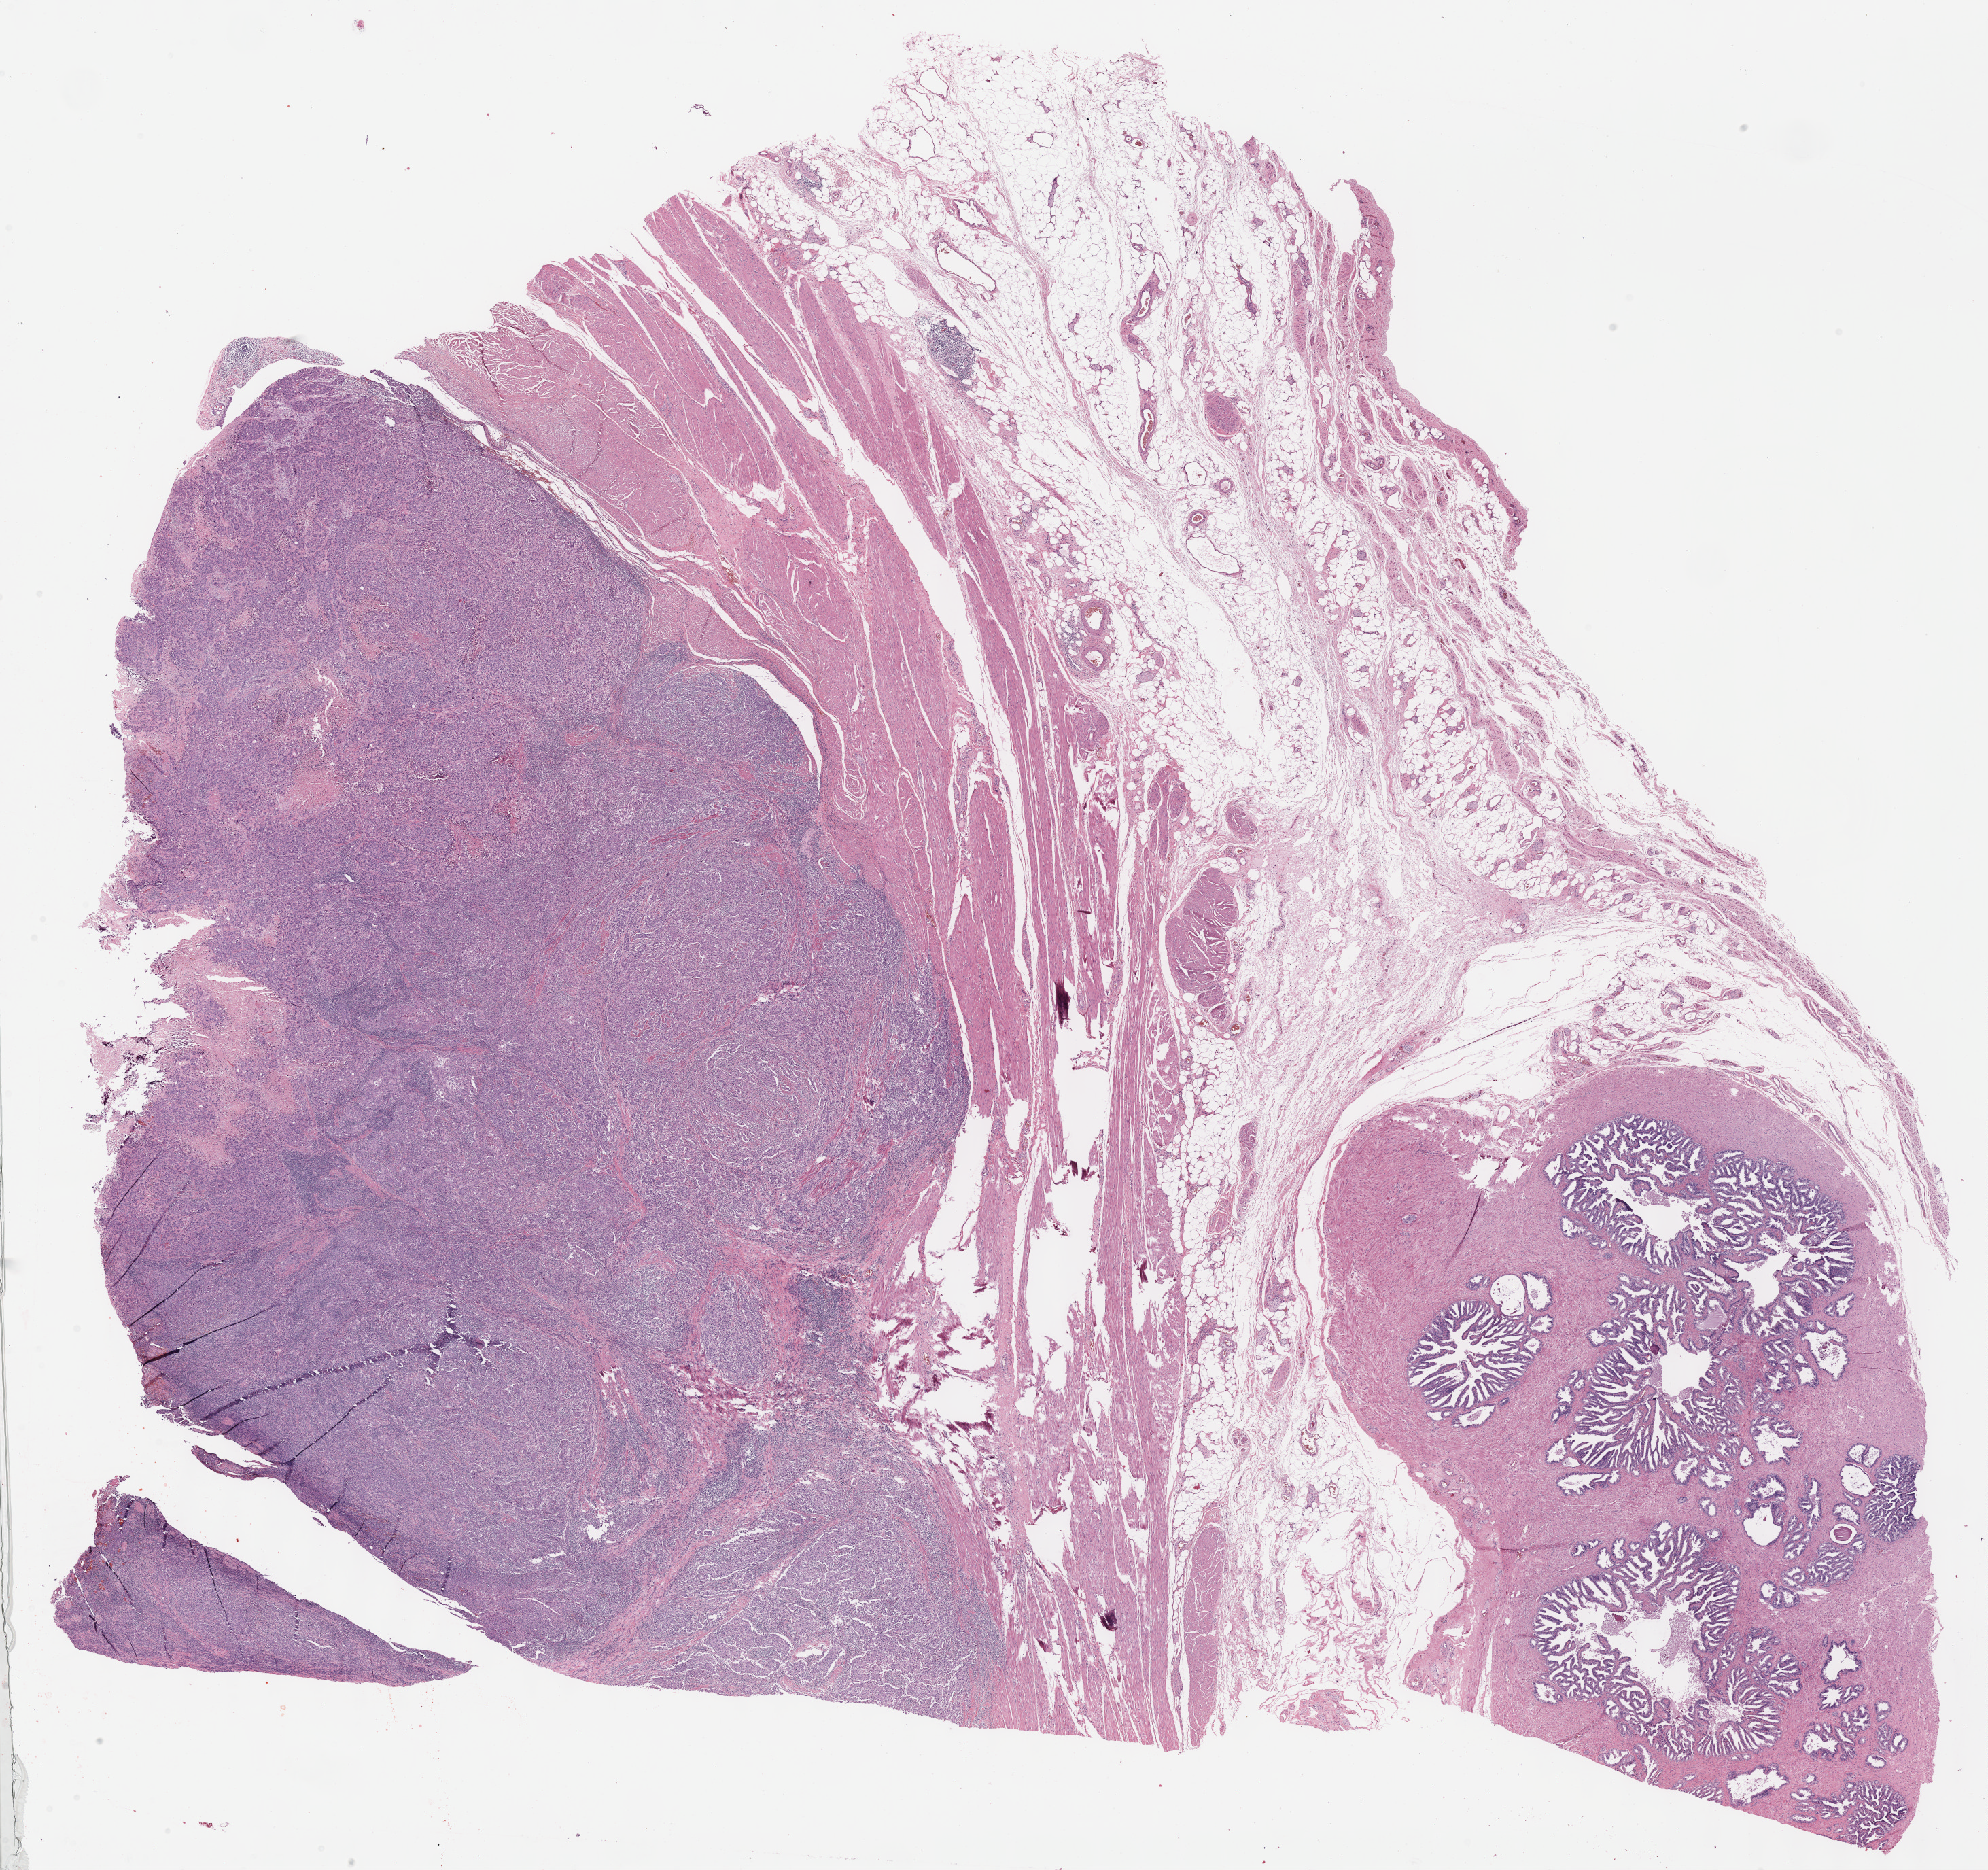
H&E whole-slide image, low-resolution overview of the scanned area, about 23.6 x 22.2 mm (from a 40x scan); formalin-fixed paraffin-embedded (FFPE) diagnostic section; sample: primary tumour, bladder. Patient: male, age at initial diagnosis 55 years. Histologic grade: high grade.
AJCC pathologic stage: II (7th edition). Pathologic diagnosis: Transitional cell carcinoma (lateral wall of bladder).